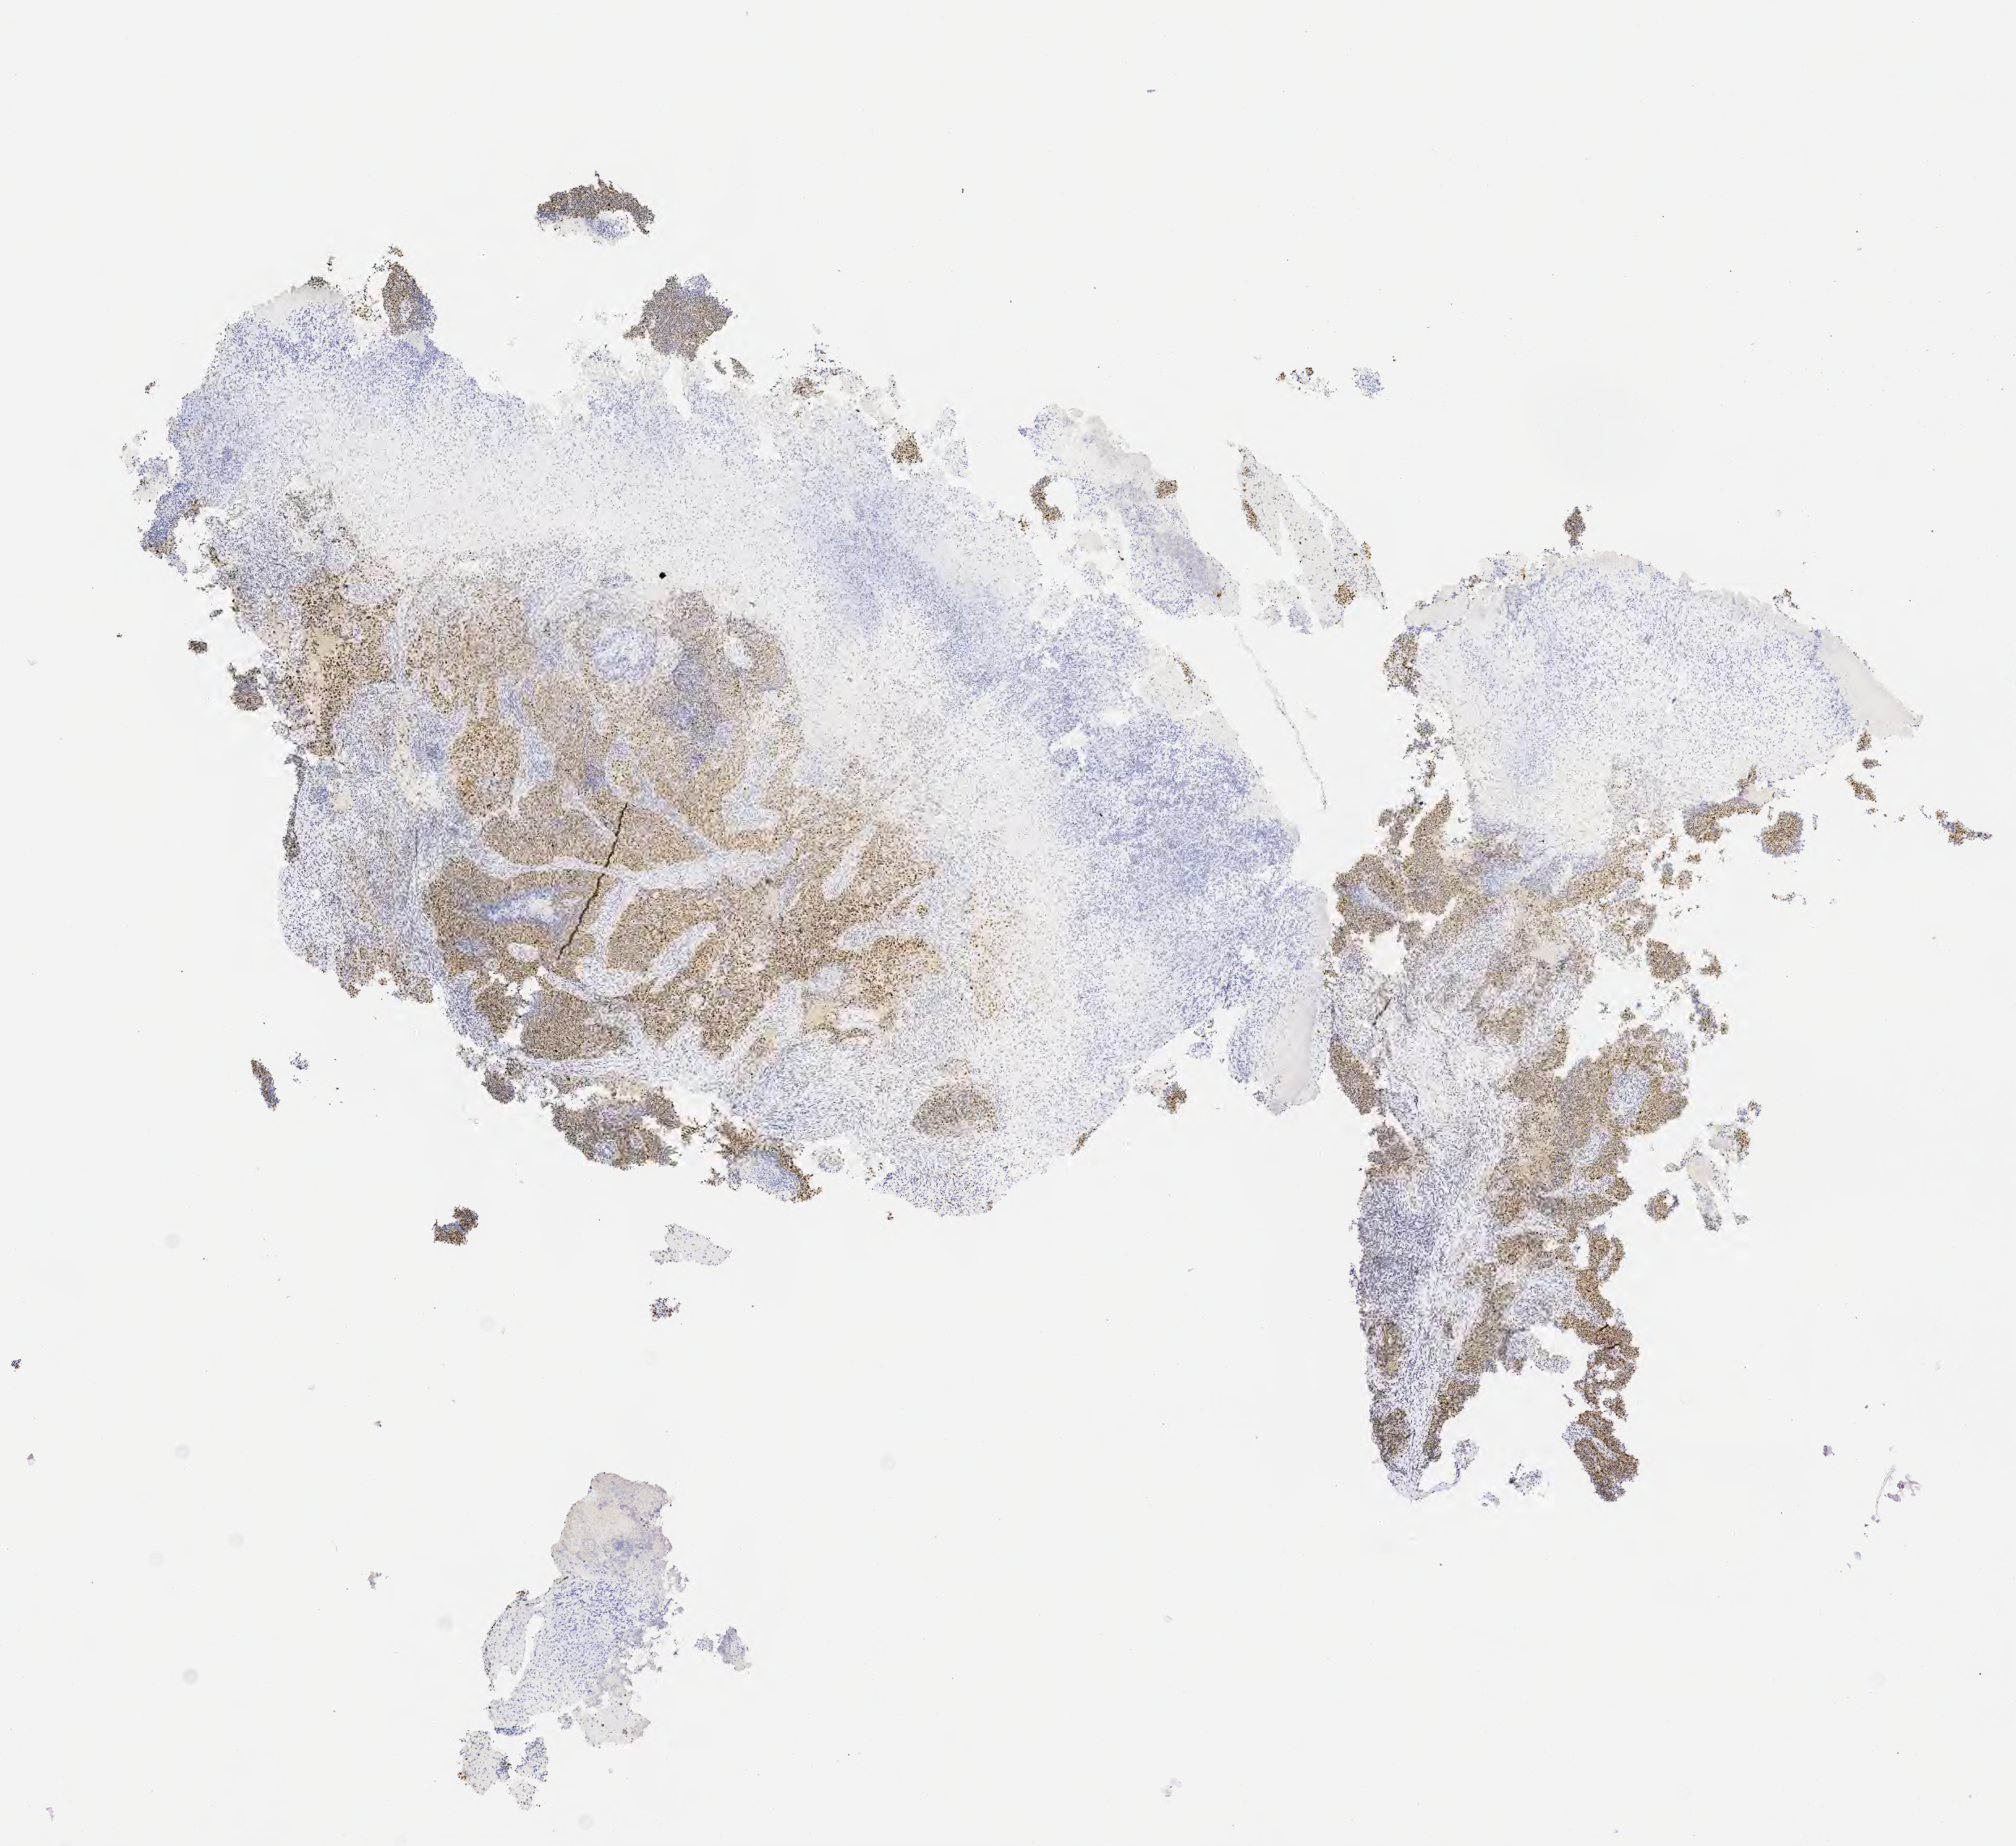
Immunohistochemistry (IHC) whole-slide image stained for p53, low-resolution overview of the scanned area, about 10.1 x 9.2 mm; tumor tissue; anatomic site: cervix. Patient: female, 65 years old.
Histologic diagnosis: Squamous cell carcinoma, large cell, nonkeratinizing, NOS.